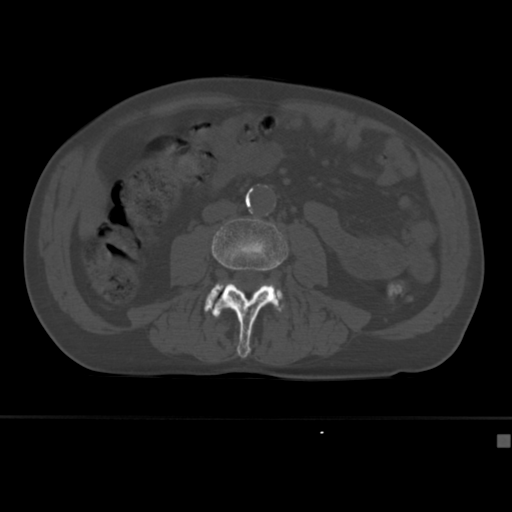
CT including the spine, one axial slice. Slice 122 of 430 in the series (ordered by position). 120 kVp. Bone window (W 1800 / L 400 HU). 1.5 mm slice thickness. 512 × 512 image matrix, field of view 337 × 337 mm. Patient: male, 64 years. From the clinical record (not read from this slice): primary cancer: uterus; vertebrae with lytic lesions (as recorded): T1, T4, T5, T7, L5.
Outlined on this slice (semi-automatic segmentation, software-assisted and operator-edited):
- L3 vertebra: bounding box <211,218,288,358> (left, top, right, bottom; pixels)
- L4 vertebra: <204,283,284,312>